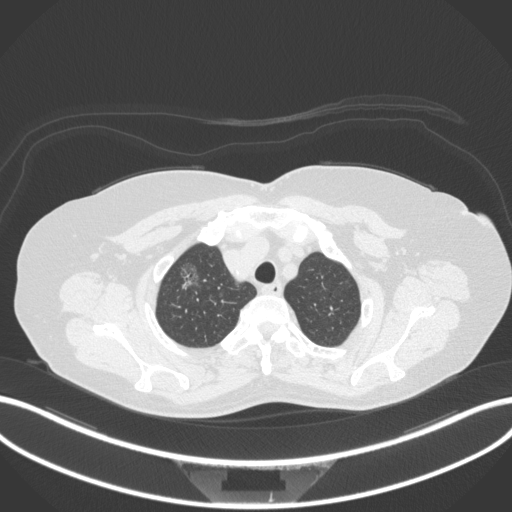
Chest CT, one axial slice. Position 302 of 365 along the scan axis. Reconstruction kernel B31f. 120 kVp. Lung window (W 1500 / L -600 HU). 1 mm slice thickness. 512 × 512 image matrix, field of view 400 × 400 mm. Female patient, age 62 years. Case-level facts recorded for this patient, not image findings: clinical TNM (as recorded): T1c N0 M0.
Annotated regions visible in this slice (rectangle marked by the reading radiologist):
- lung tumour (recorded histology: adenocarcinoma): box from (x=173, y=258) to (x=206, y=300) px